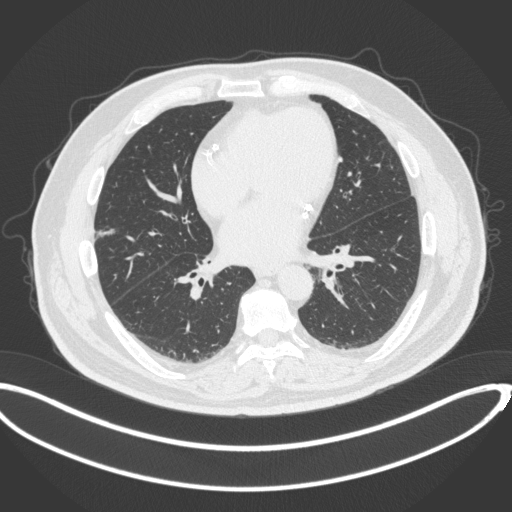
Chest CT, one axial slice. Position 144 of 342 along the scan axis. Reconstruction kernel B31f. 120 kVp. Lung window (W 1500 / L -600 HU). 1 mm slice thickness. 512 × 512 image matrix, field of view 427 × 427 mm. Male patient, age 68 years. Case-level facts recorded for this patient, not image findings: clinical TNM (as recorded): T1c N0 M0; histopathological grade: G2.
Annotated regions visible in this slice (rectangle marked by the reading radiologist):
- lung tumour (recorded histology: adenocarcinoma): box from (x=99, y=227) to (x=113, y=239) px